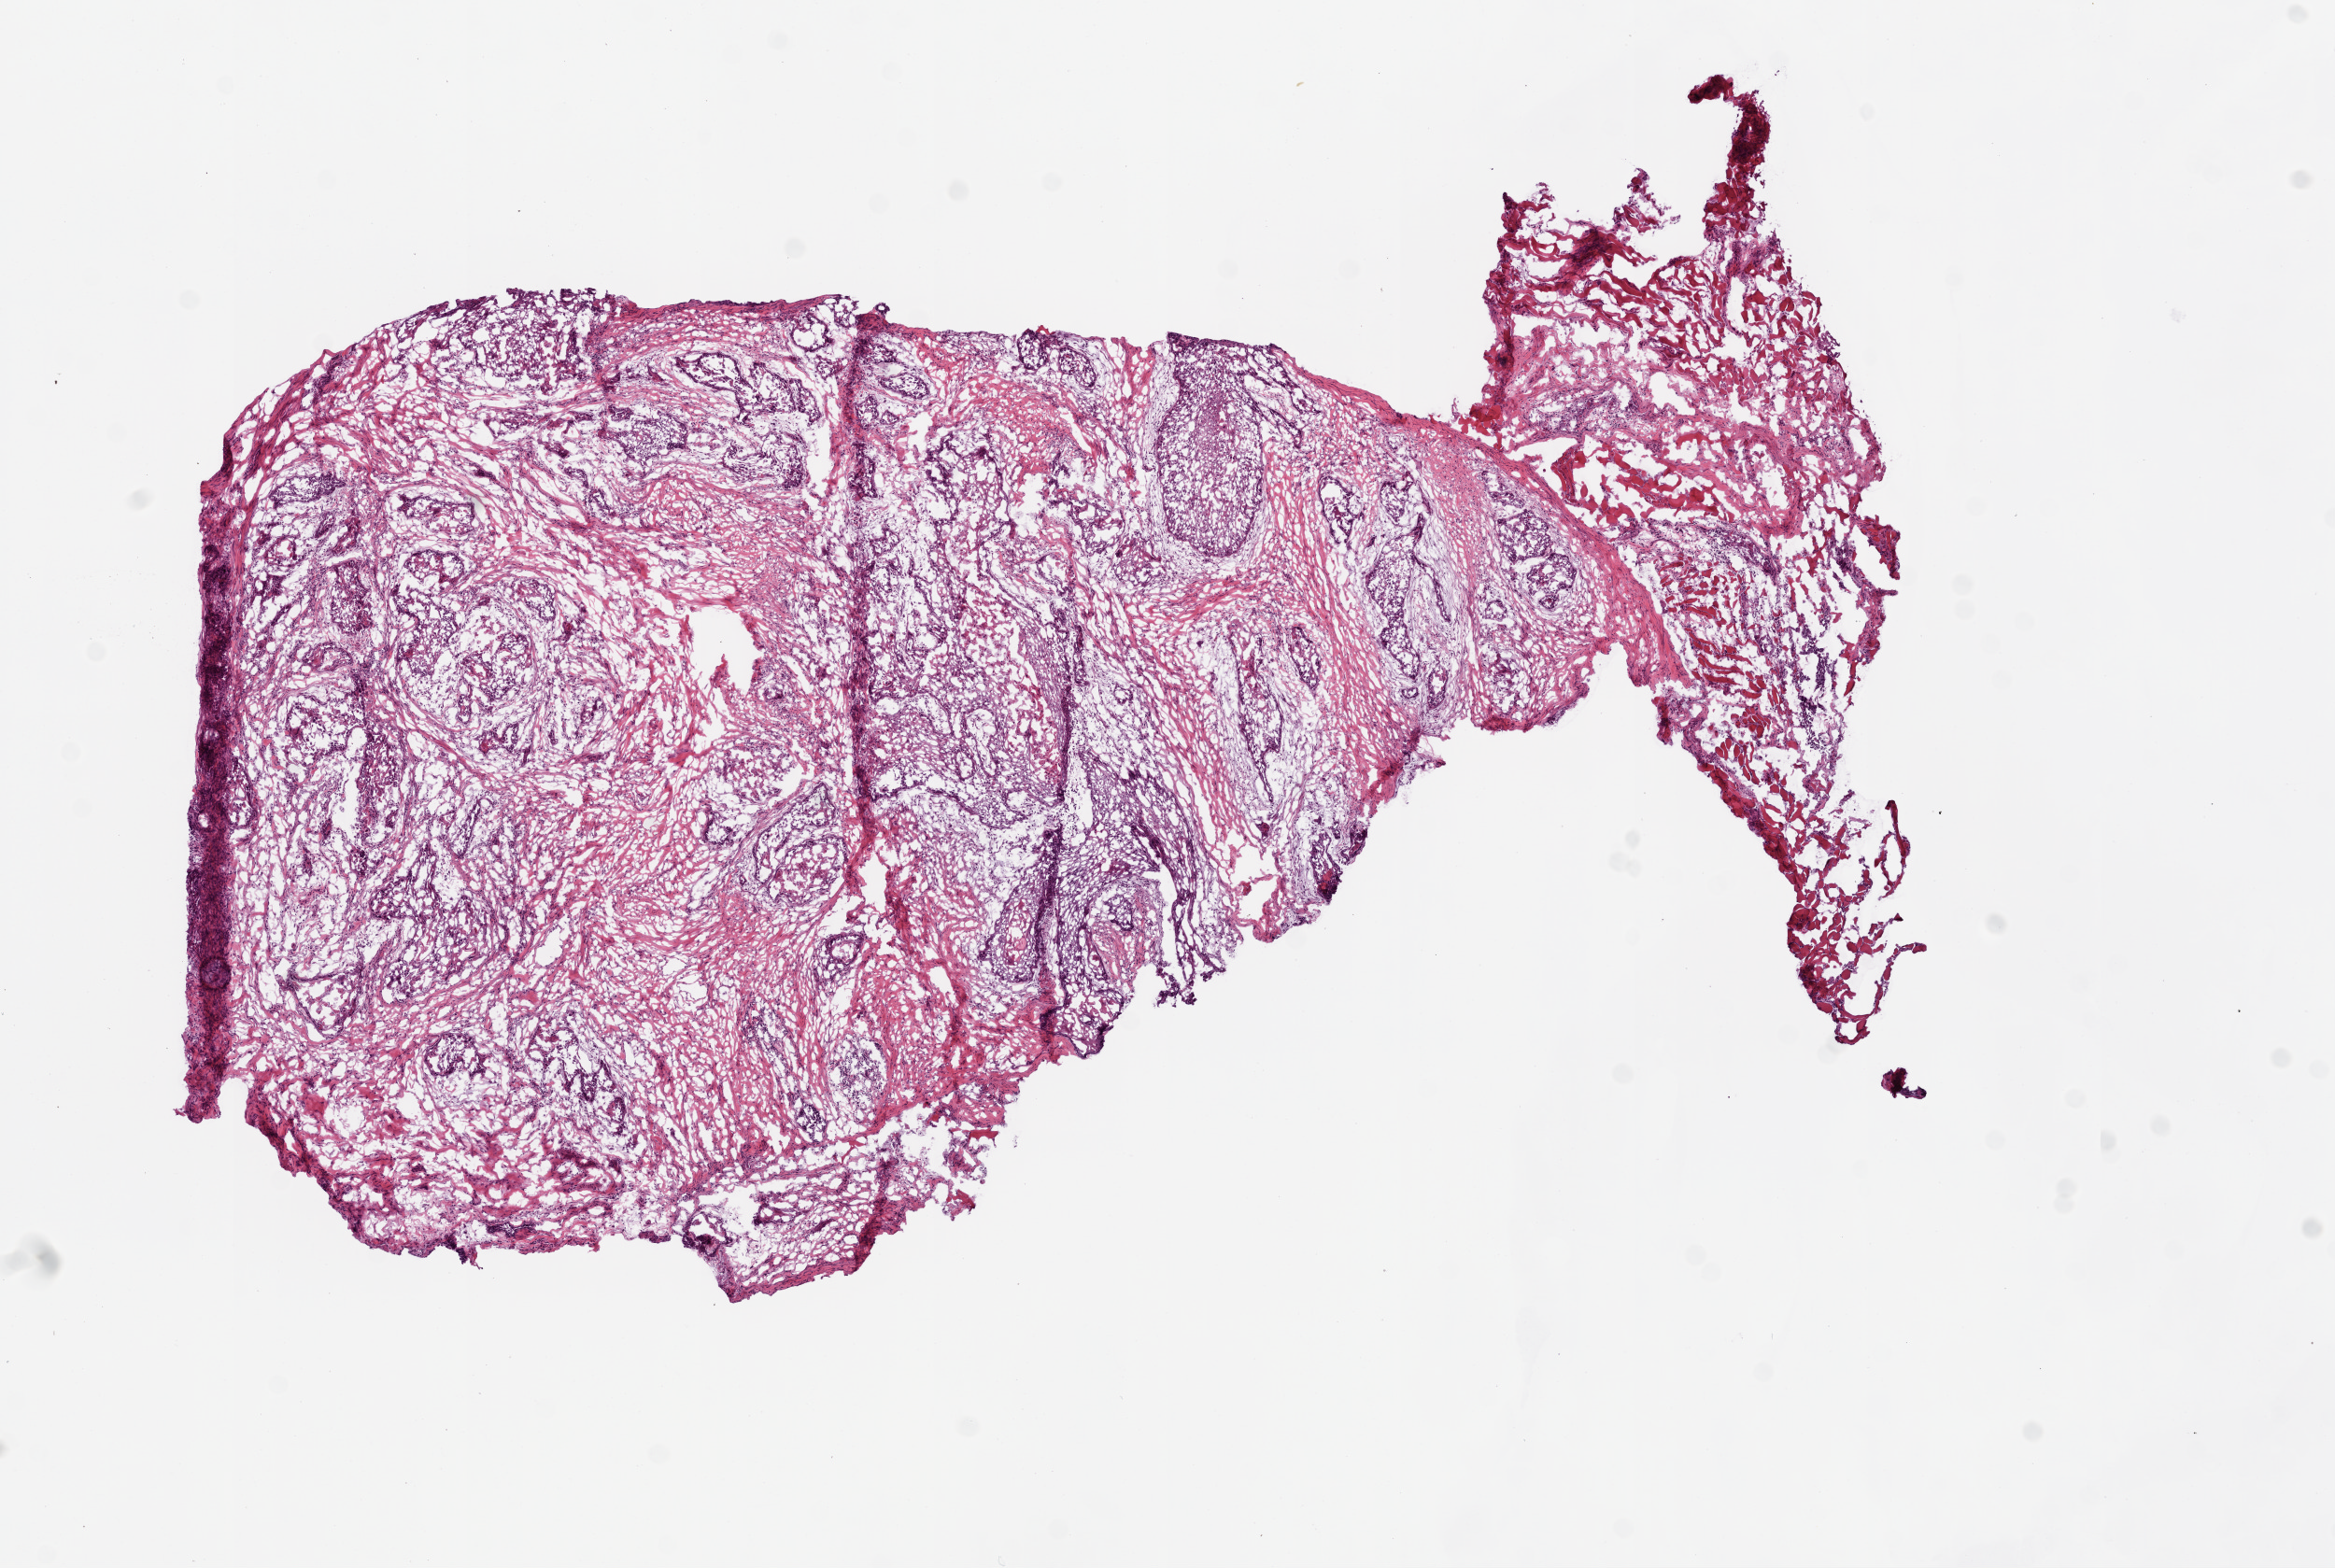
Whole-slide histology image, H&E-stained — whole scanned area (about 10.0 x 6.7 mm, slide scanned at 20x) shown as a low-resolution overview. Frozen section from the top of the tissue portion. Sample: primary tumour, head and neck. Male, age 55 years at initial diagnosis. Histologic grade: G2 (moderately differentiated). Pathologist review of this section (percent, as recorded): tumour cells 75%, tumour nuclei 70%, normal cells 10%, stromal cells 15%, necrosis 0%.
• AJCC pathologic stage: IVA (6th edition)
• histologic diagnosis: Squamous cell carcinoma, NOS (floor of mouth, NOS)